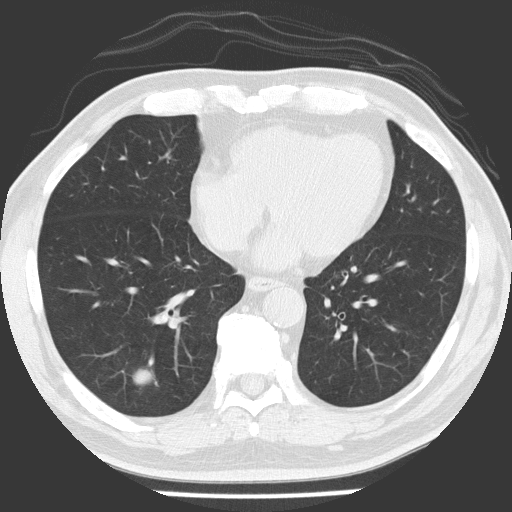
Low-dose screening chest CT, one axial slice. Position 60 of 154 along the scan axis. Lung window (W 1500 / L -600 HU). 2 mm slice thickness. 512 × 512 image matrix, field of view 311 × 311 mm.
Outlined on this slice (outlined manually by an expert reader):
- lesion 1 (tumor, lower lobe of right lung): bounding box [x1, y1, x2, y2] px = [133, 369, 152, 384]